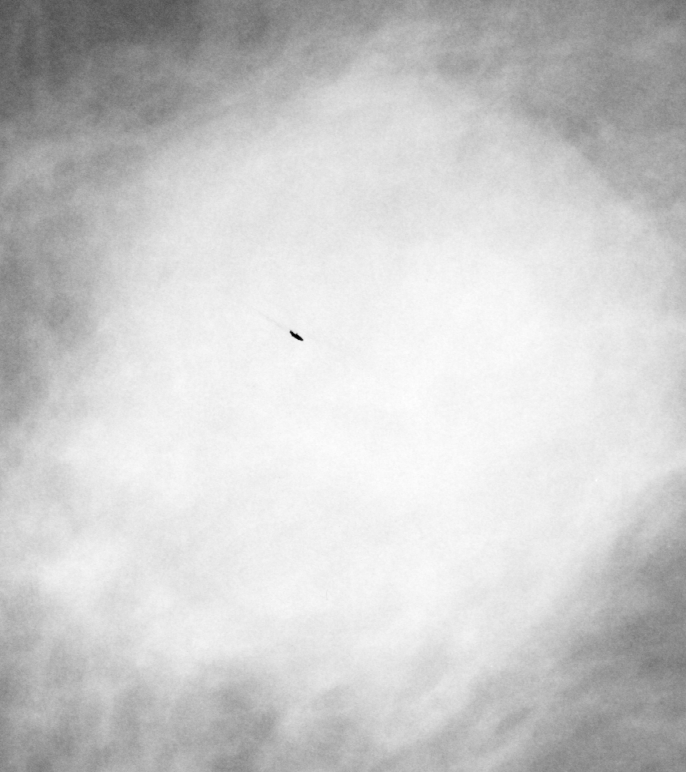
Cropped region of a digitized screen-film mammogram centred on a radiologist-marked abnormality, right breast, MLO view.
Marked abnormality: mass, shape lobulated, margins microlobulated; BI-RADS assessment category 5; subtlety rating 5 on a 1 (subtle) to 5 (obvious) scale; pathology result (as recorded, not read from the image): malignant.